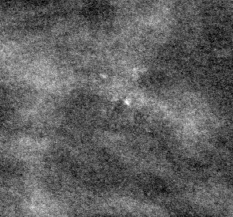
Cropped region of a digitized screen-film mammogram centred on a radiologist-marked abnormality, left breast, CC view, BI-RADS breast density category 2 (scale 1–4).
- Calcifications, morphology pleomorphic, distribution clustered; BI-RADS assessment category 4; subtlety rating 3 on a 1 (subtle) to 5 (obvious) scale; pathology result (as recorded, not read from the image): benign.